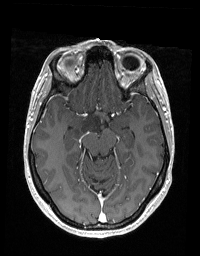
Brain MRI from a brain-tumour surgery series, one axial slice. Slice 115 of 192 in the series (ordered by position). T1-weighted post-contrast. 200 × 256 image matrix, field of view 195 × 250 mm. Case-level facts recorded for this patient, not image findings: histopathology: Glioblastoma; WHO grade: 2; IDH mutation: no; tumour location: Right Skull Base Temporal.
Outlined on this slice (outlined manually by an expert reader):
- tumour: bounding box <73,114,100,138> (left, top, right, bottom; pixels)